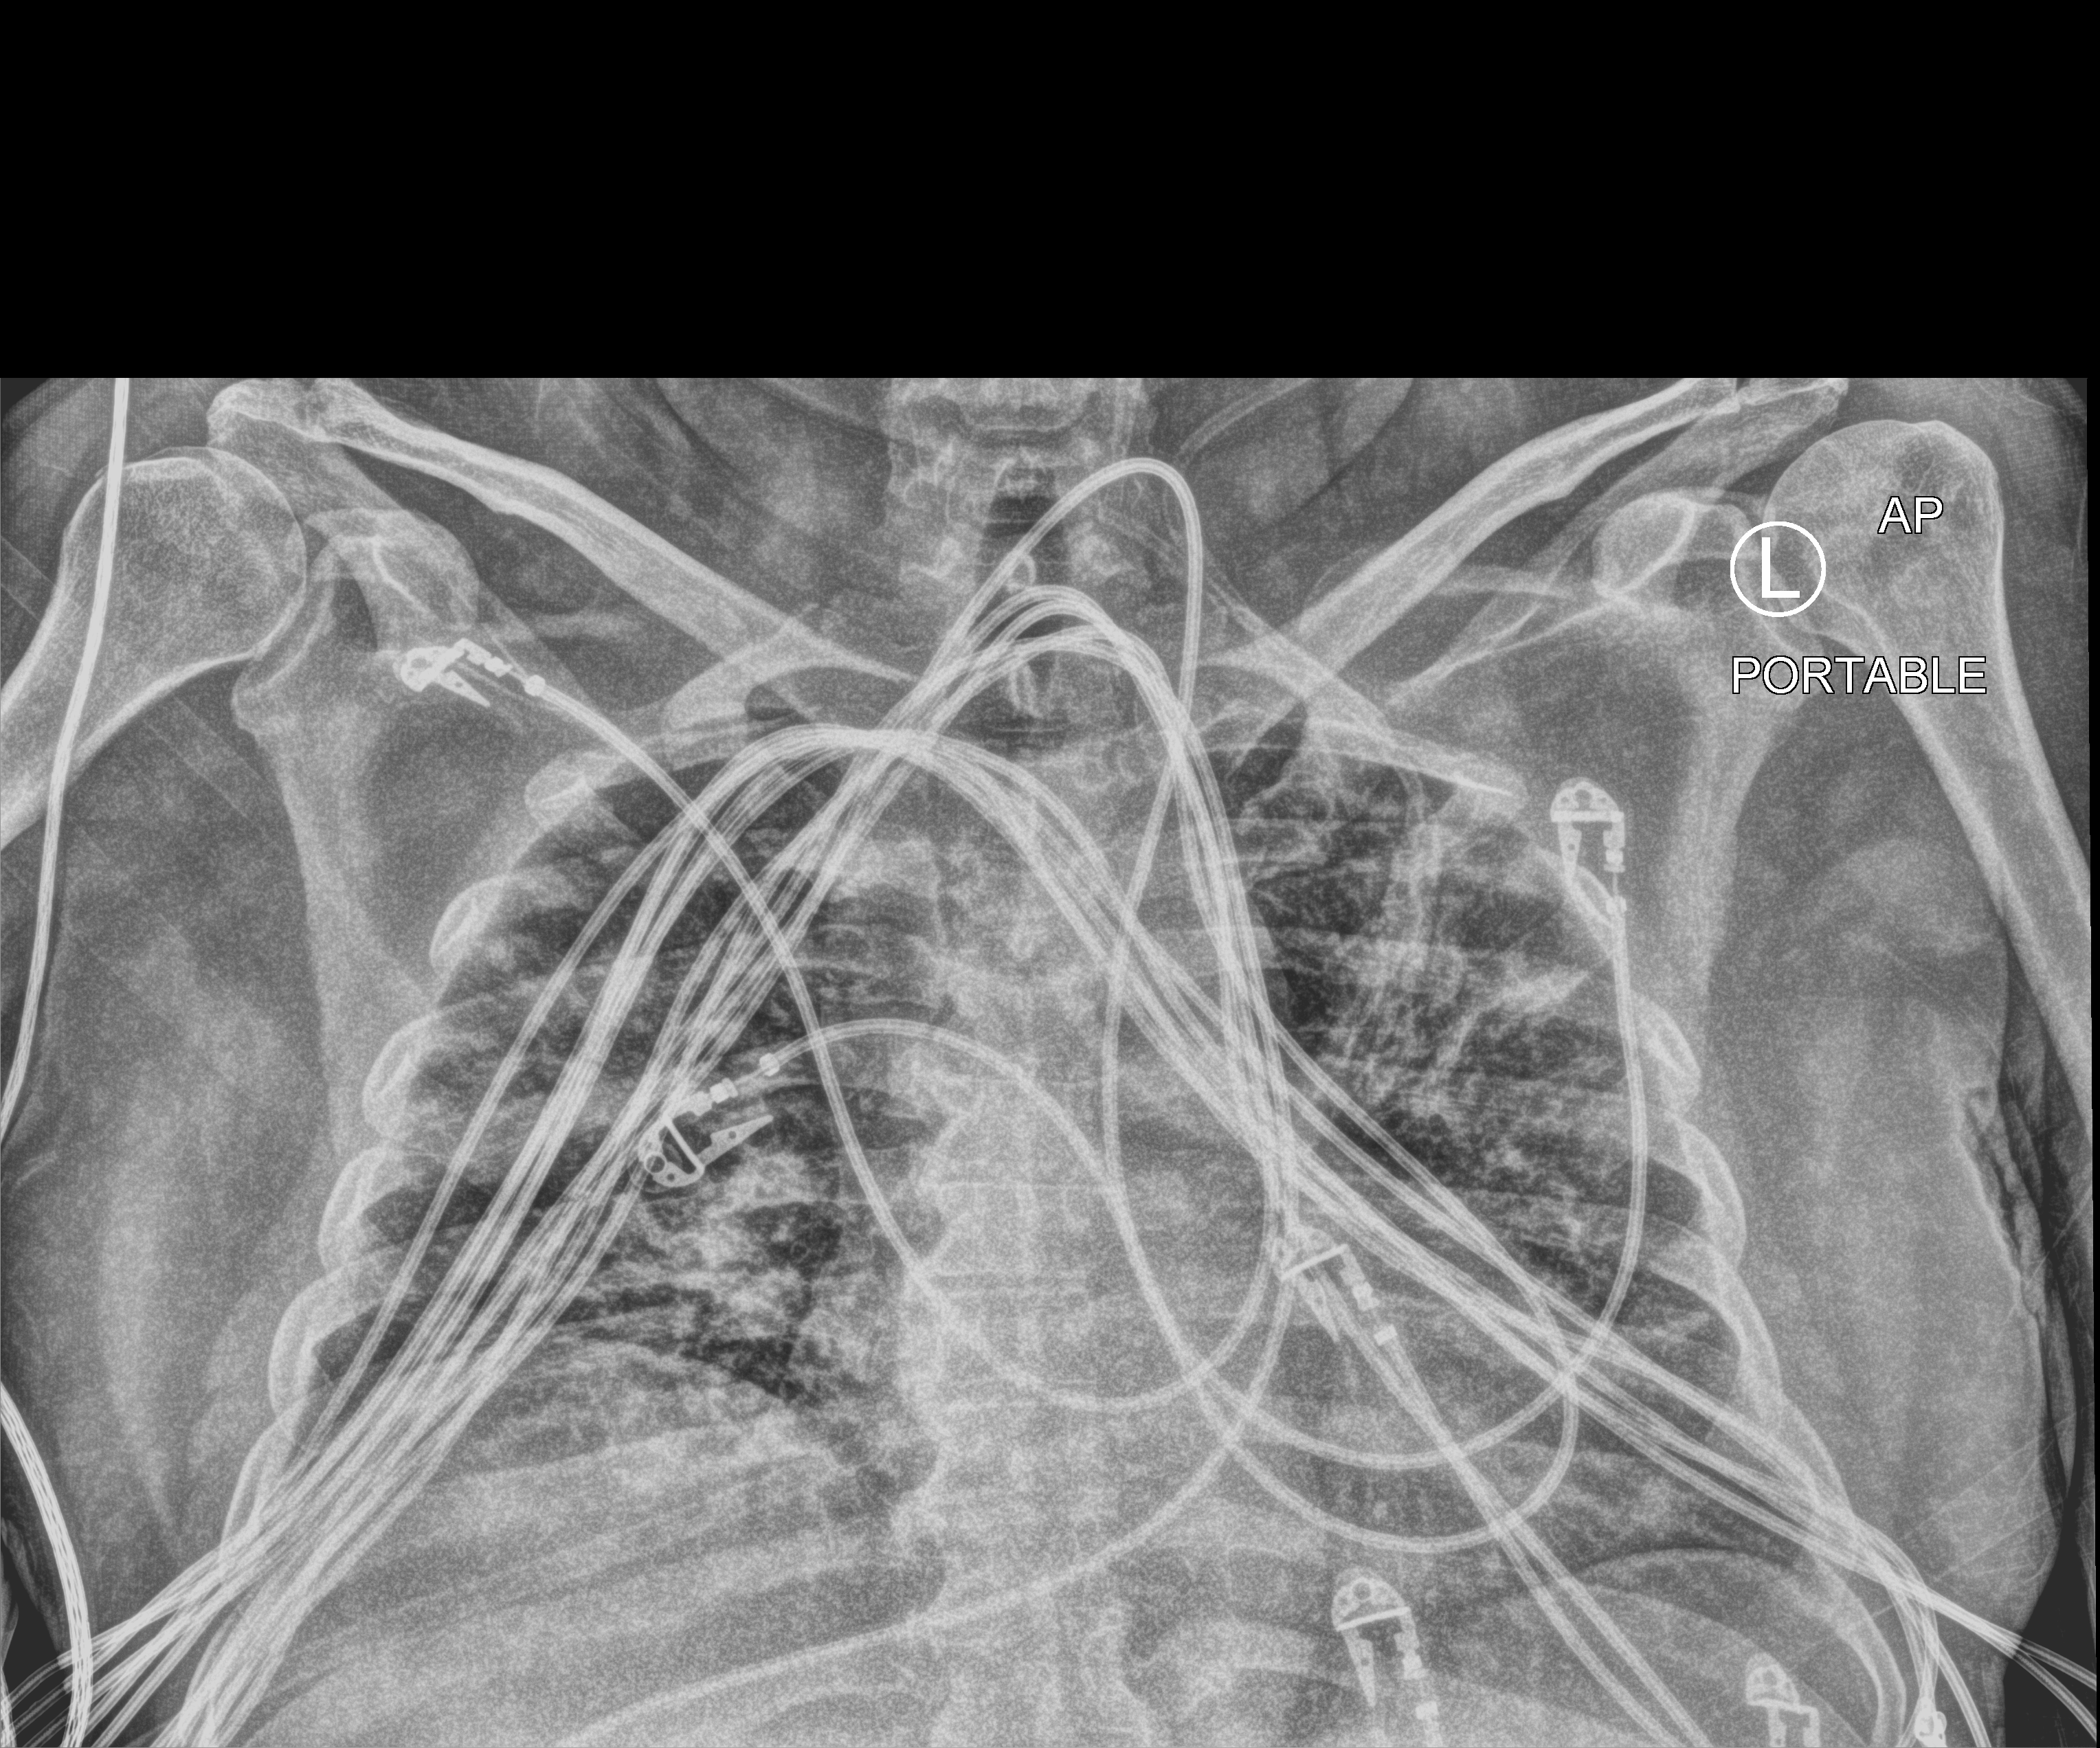
Bedside chest radiograph (computed radiography), anteroposterior (AP) projection. Patient hospitalised with COVID-19; male, aged 18–59 years.
Admission-level facts for this patient (not findings on this image; timing relative to this image not recorded): diabetes (admission record): yes; mechanically ventilated during this hospital stay: yes.